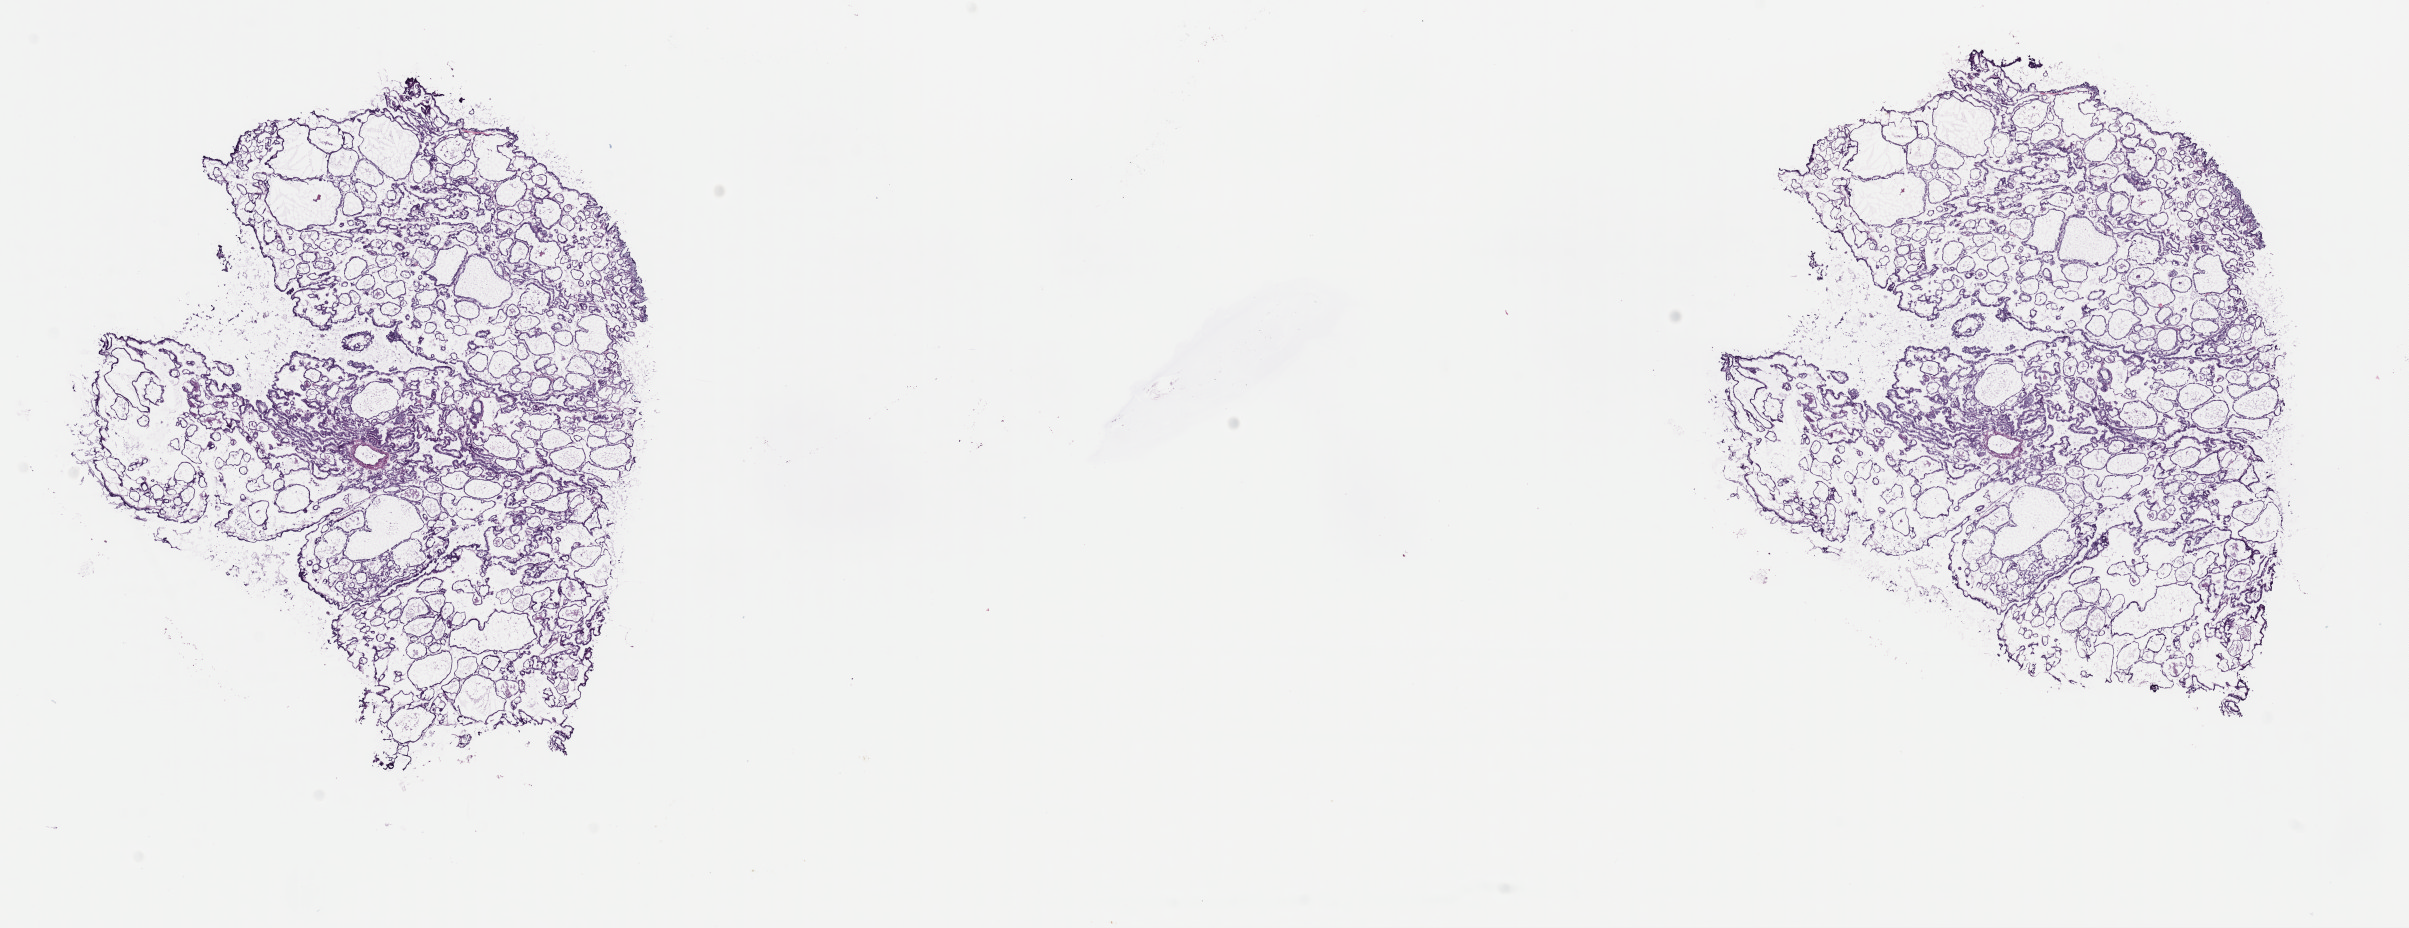
Whole-slide histology image, H&E-stained — shown as a low-resolution overview of the whole scanned area (about 19.0 x 7.3 mm, acquisition: 40x scan), frozen section from the top of the tissue portion, thyroid, primary tumour sample. Female patient; age at initial diagnosis 46 years.
Histologic diagnosis: Papillary adenocarcinoma, NOS (thyroid gland).